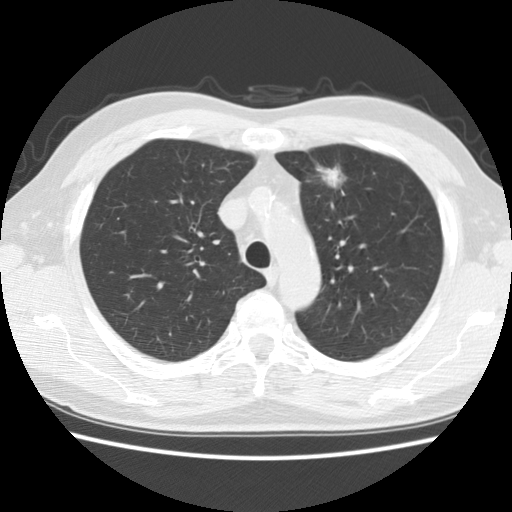
Low-dose screening chest CT, axial slice. Second screening round (one year after baseline). Lung window (W 1500 / L -600 HU). Standard (soft-tissue) reconstruction kernel (STANDARD). Male, age 63 years at enrolment.
• Expert reader's lesion annotation, box from (x=299, y=148) to (x=357, y=203) px.
• Screening reader's record for this exam (one nodule recorded; not confirmed to be the boxed lesion): non-calcified nodule or mass ≥4 mm, left upper lobe, 23 × 18 mm, spiculated (stellate) margins, soft tissue attenuation, pre-existing on the prior screen: yes; interval growth: yes.
• Official screen result: positive, other.
• Lung cancer was diagnosed 83 days after this screen: adenocarcinoma, NOS, left upper lobe, moderately differentiated (G2), stage IA (AJCC 6th edition), 14 mm at pathology.